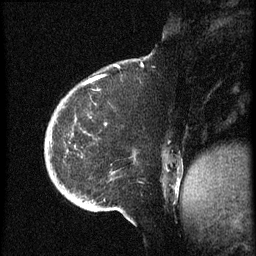
Breast MRI (dynamic contrast-enhanced), one sagittal slice; slice 15 of 60 in the series (ordered by position); dynamic contrast-enhanced series, image 2 of 3 at this slice position (ordered by acquisition); 1.5 T; TE 4.2 ms, TR 8.4 ms; 2.5 mm slice thickness; 256 × 256 image matrix, field of view 200 × 200 mm. Patient: female, 38 years. Case-level facts recorded for this patient, not image findings: setting: breast cancer imaged before/during neoadjuvant chemotherapy; receptor status: HER2-positive.
Annotated regions visible in this slice (semi-automatically segmented with operator editing):
- analysis volume of interest (the breast-tissue region the enhancement analysis was run in; not a lesion): bounding box (x1, y1, x2, y2) in pixels: (45, 74, 173, 202)
- tumour enhancement mask (voxels above the 70 % enhancement threshold inside the analysis volume of interest): (95, 78, 100, 81)